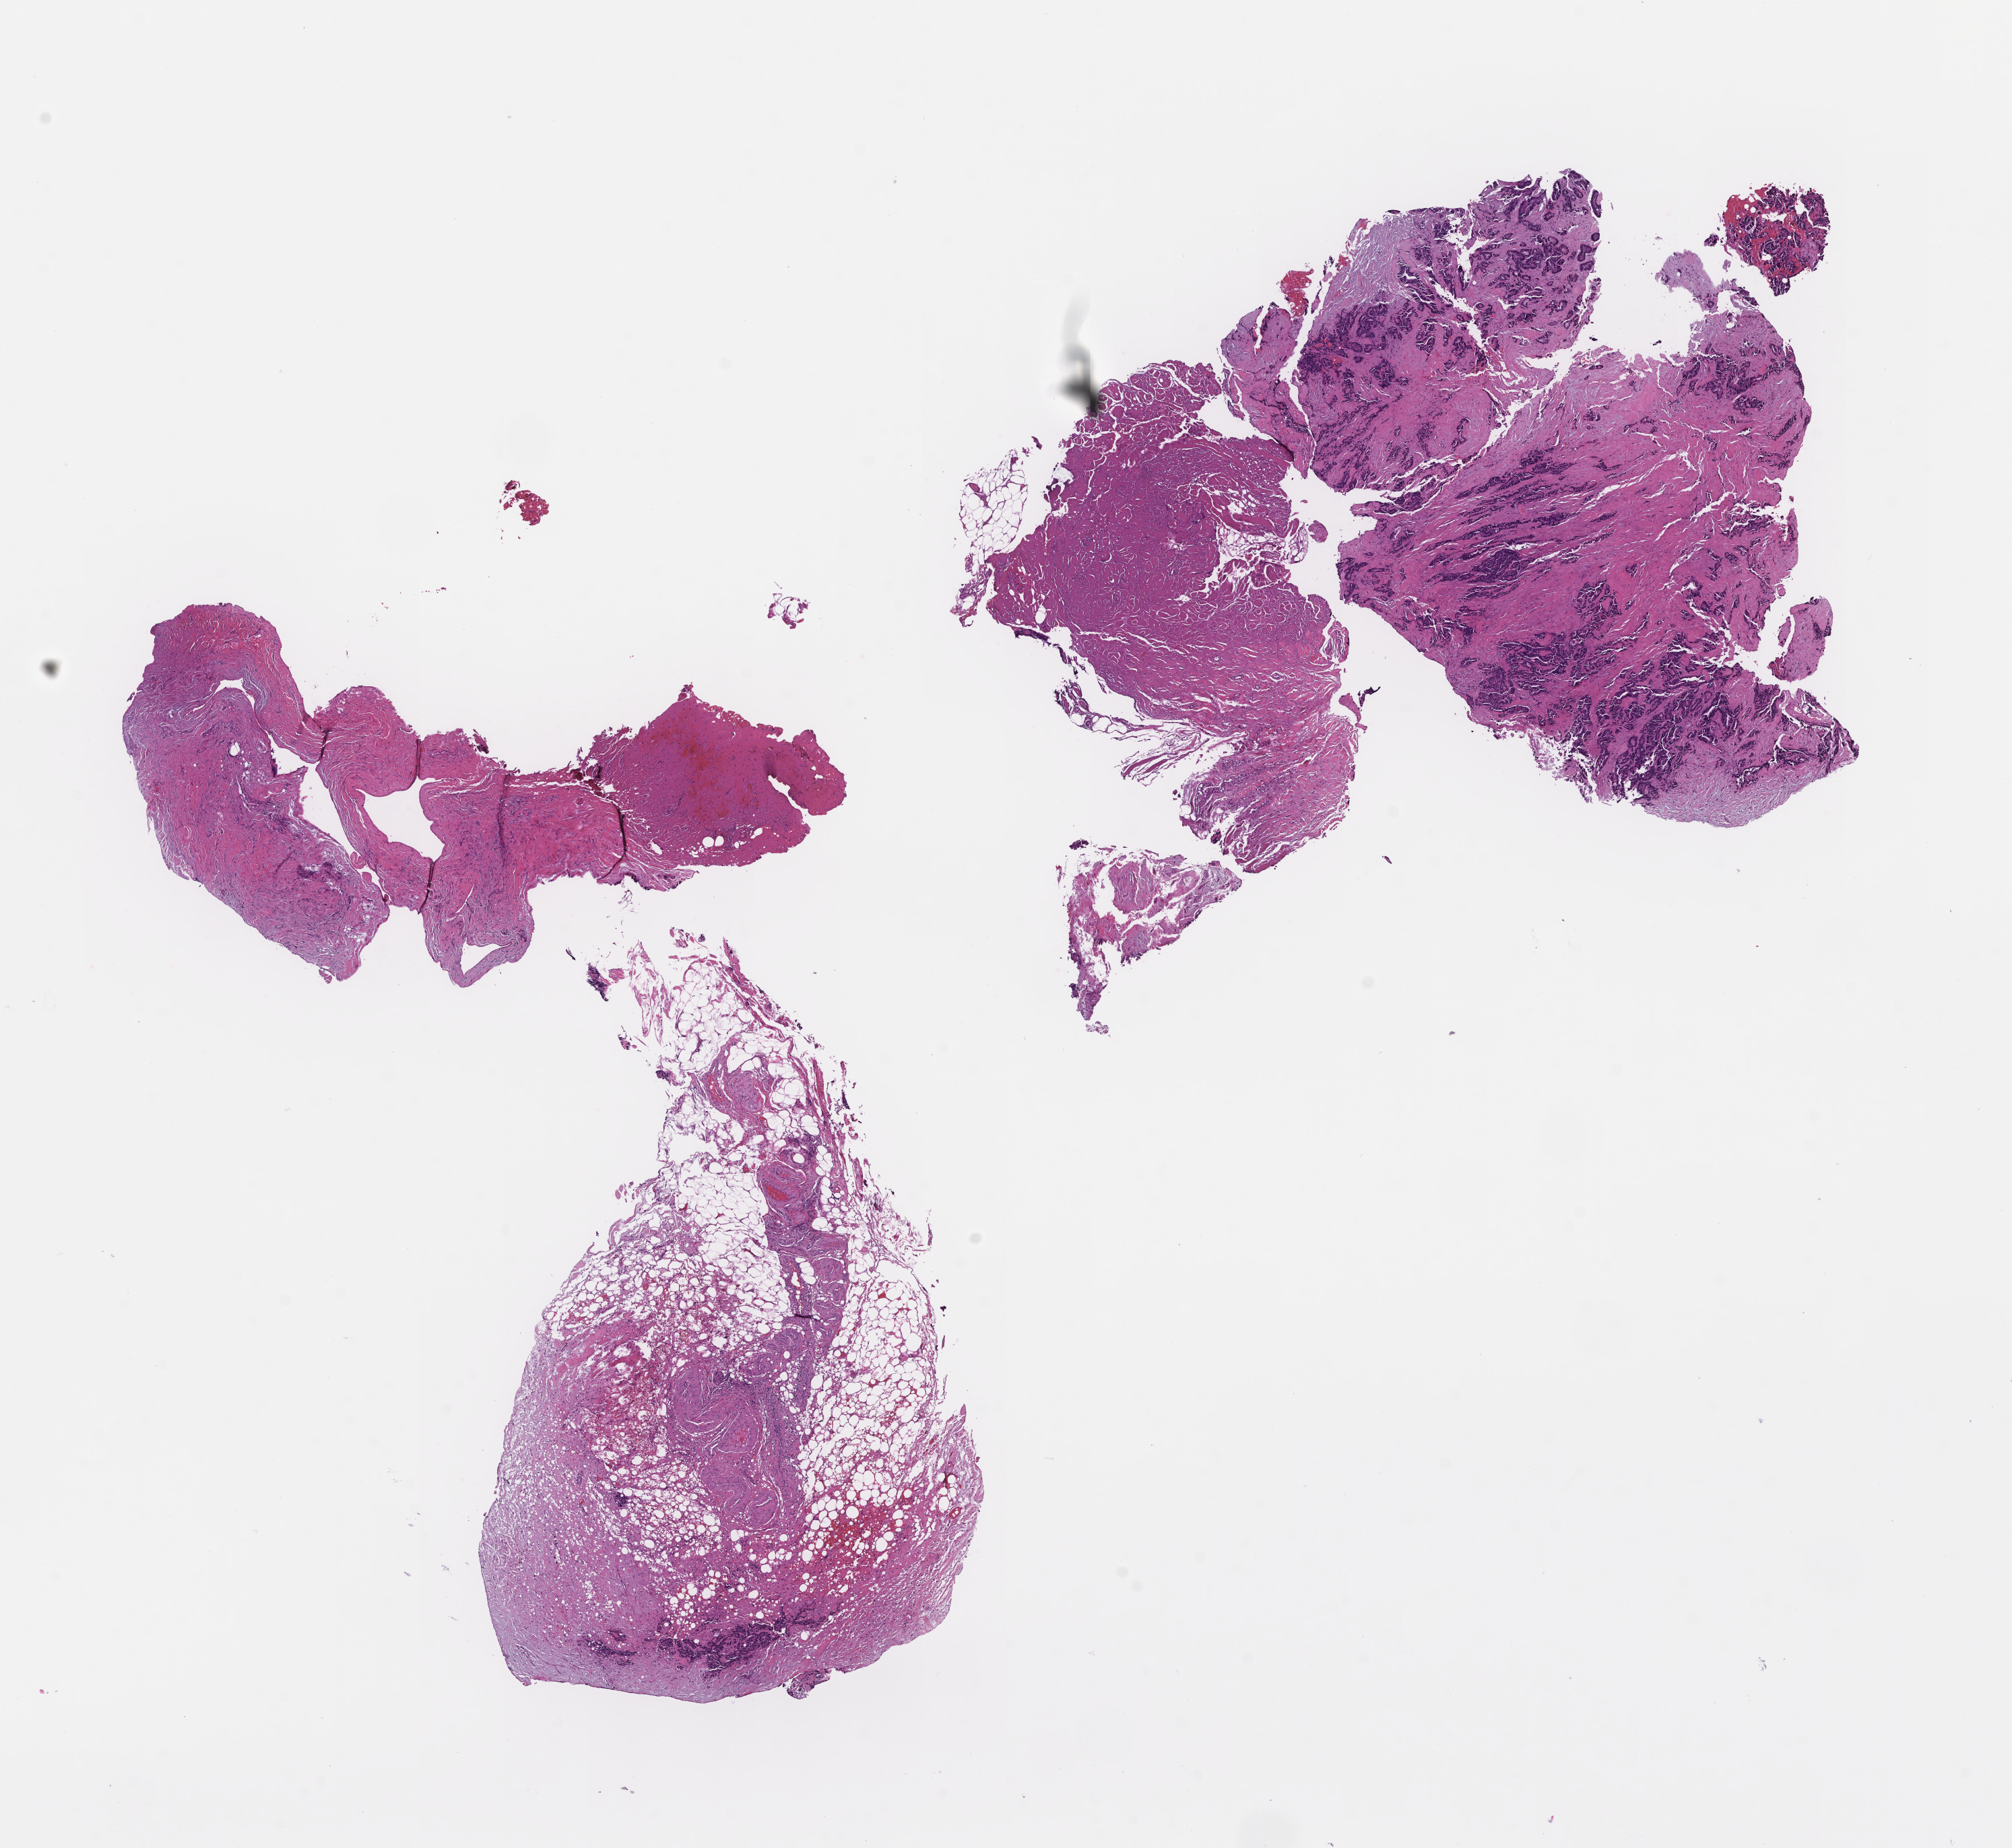
Whole-slide image, H&E stain — shown as a low-resolution overview of the whole scanned area (about 12.1 x 11.1 mm); formalin-fixed paraffin-embedded section. Female patient.
This section: metastasis (sampled organ not recorded). Primary diagnosis of the patient: Colorectal Carcinoma.